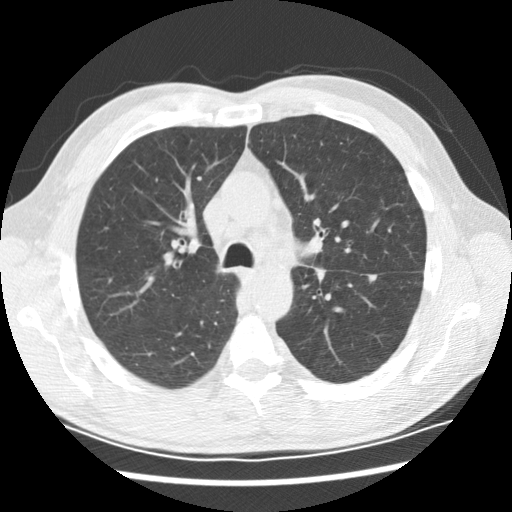
Low-dose screening chest CT, one axial slice; slice 136 of 208 in the series (ordered by position); reconstruction kernel STANDARD; 120 kVp; lung window (W 1500 / L -600 HU); 2.5 mm slice thickness; 512 × 512 image matrix, field of view 340 × 340 mm.
Outlined on this slice (manually delineated by an expert):
- lesion 2 (tumor, lower lobe of left lung): bounding box (x1, y1, x2, y2) in pixels: (368, 275, 379, 282)